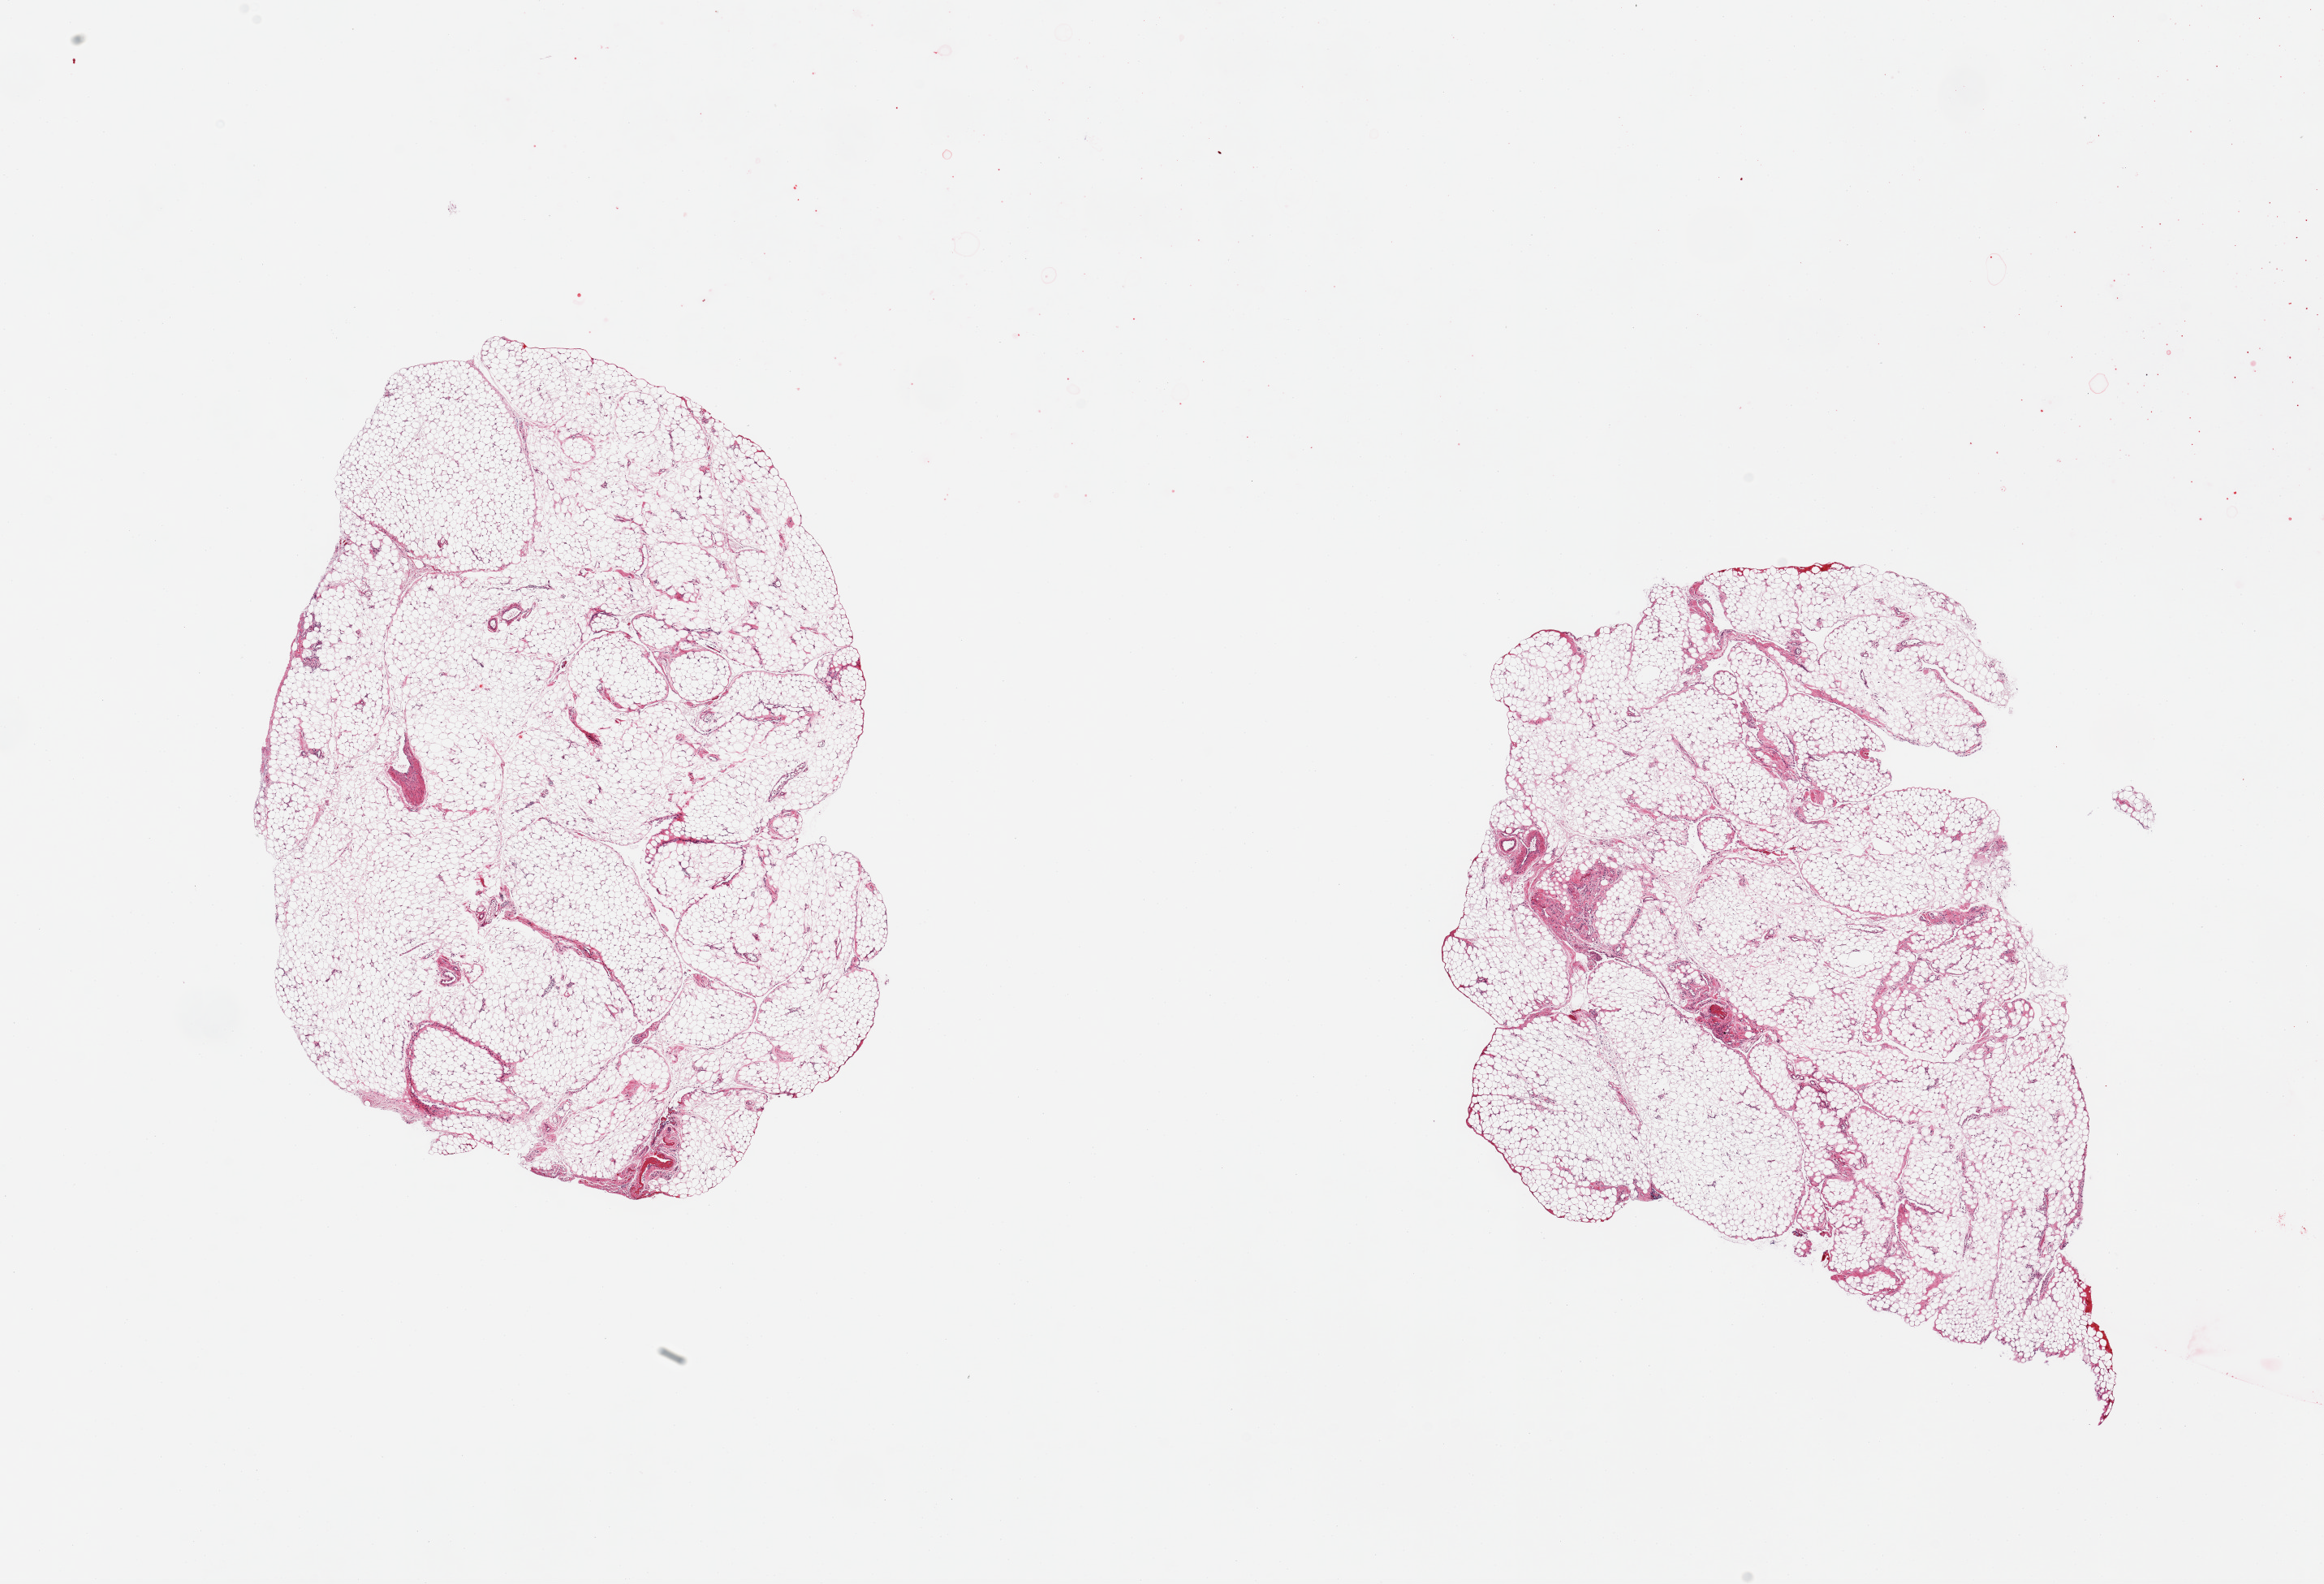
Digitized H&E-stained section, whole scanned area (about 22.6 x 15.4 mm) shown as a low-resolution overview. PAXgene-fixed, paraffin-embedded tissue. Section of omentum (target tissue). Tissue donor sample.
Pathologist's review note for this sample: 2 pieces.